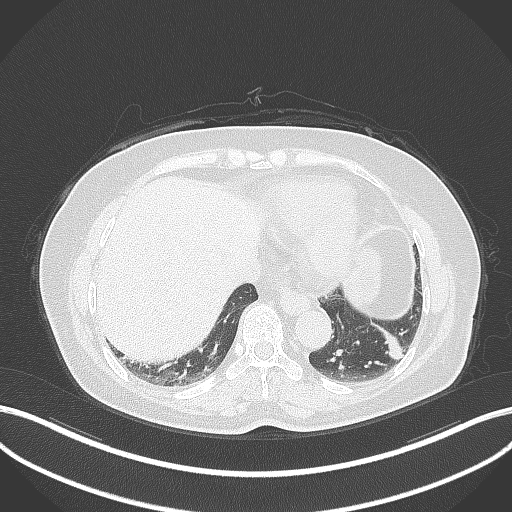
Chest CT, one axial slice. Slice 103 of 311 in the series (ordered by position). Reconstruction kernel B70f. Lung window (W 1500 / L -600 HU). 512 × 512 image matrix. Patient: female, 59 years. Case-level facts recorded for this patient, not image findings: clinical TNM (as recorded): T2a N0 M0.
Outlined on this slice (rectangle marked by the reading radiologist):
- lung tumour (recorded histology: adenocarcinoma): bounding box <367,315,408,366> (left, top, right, bottom; pixels)